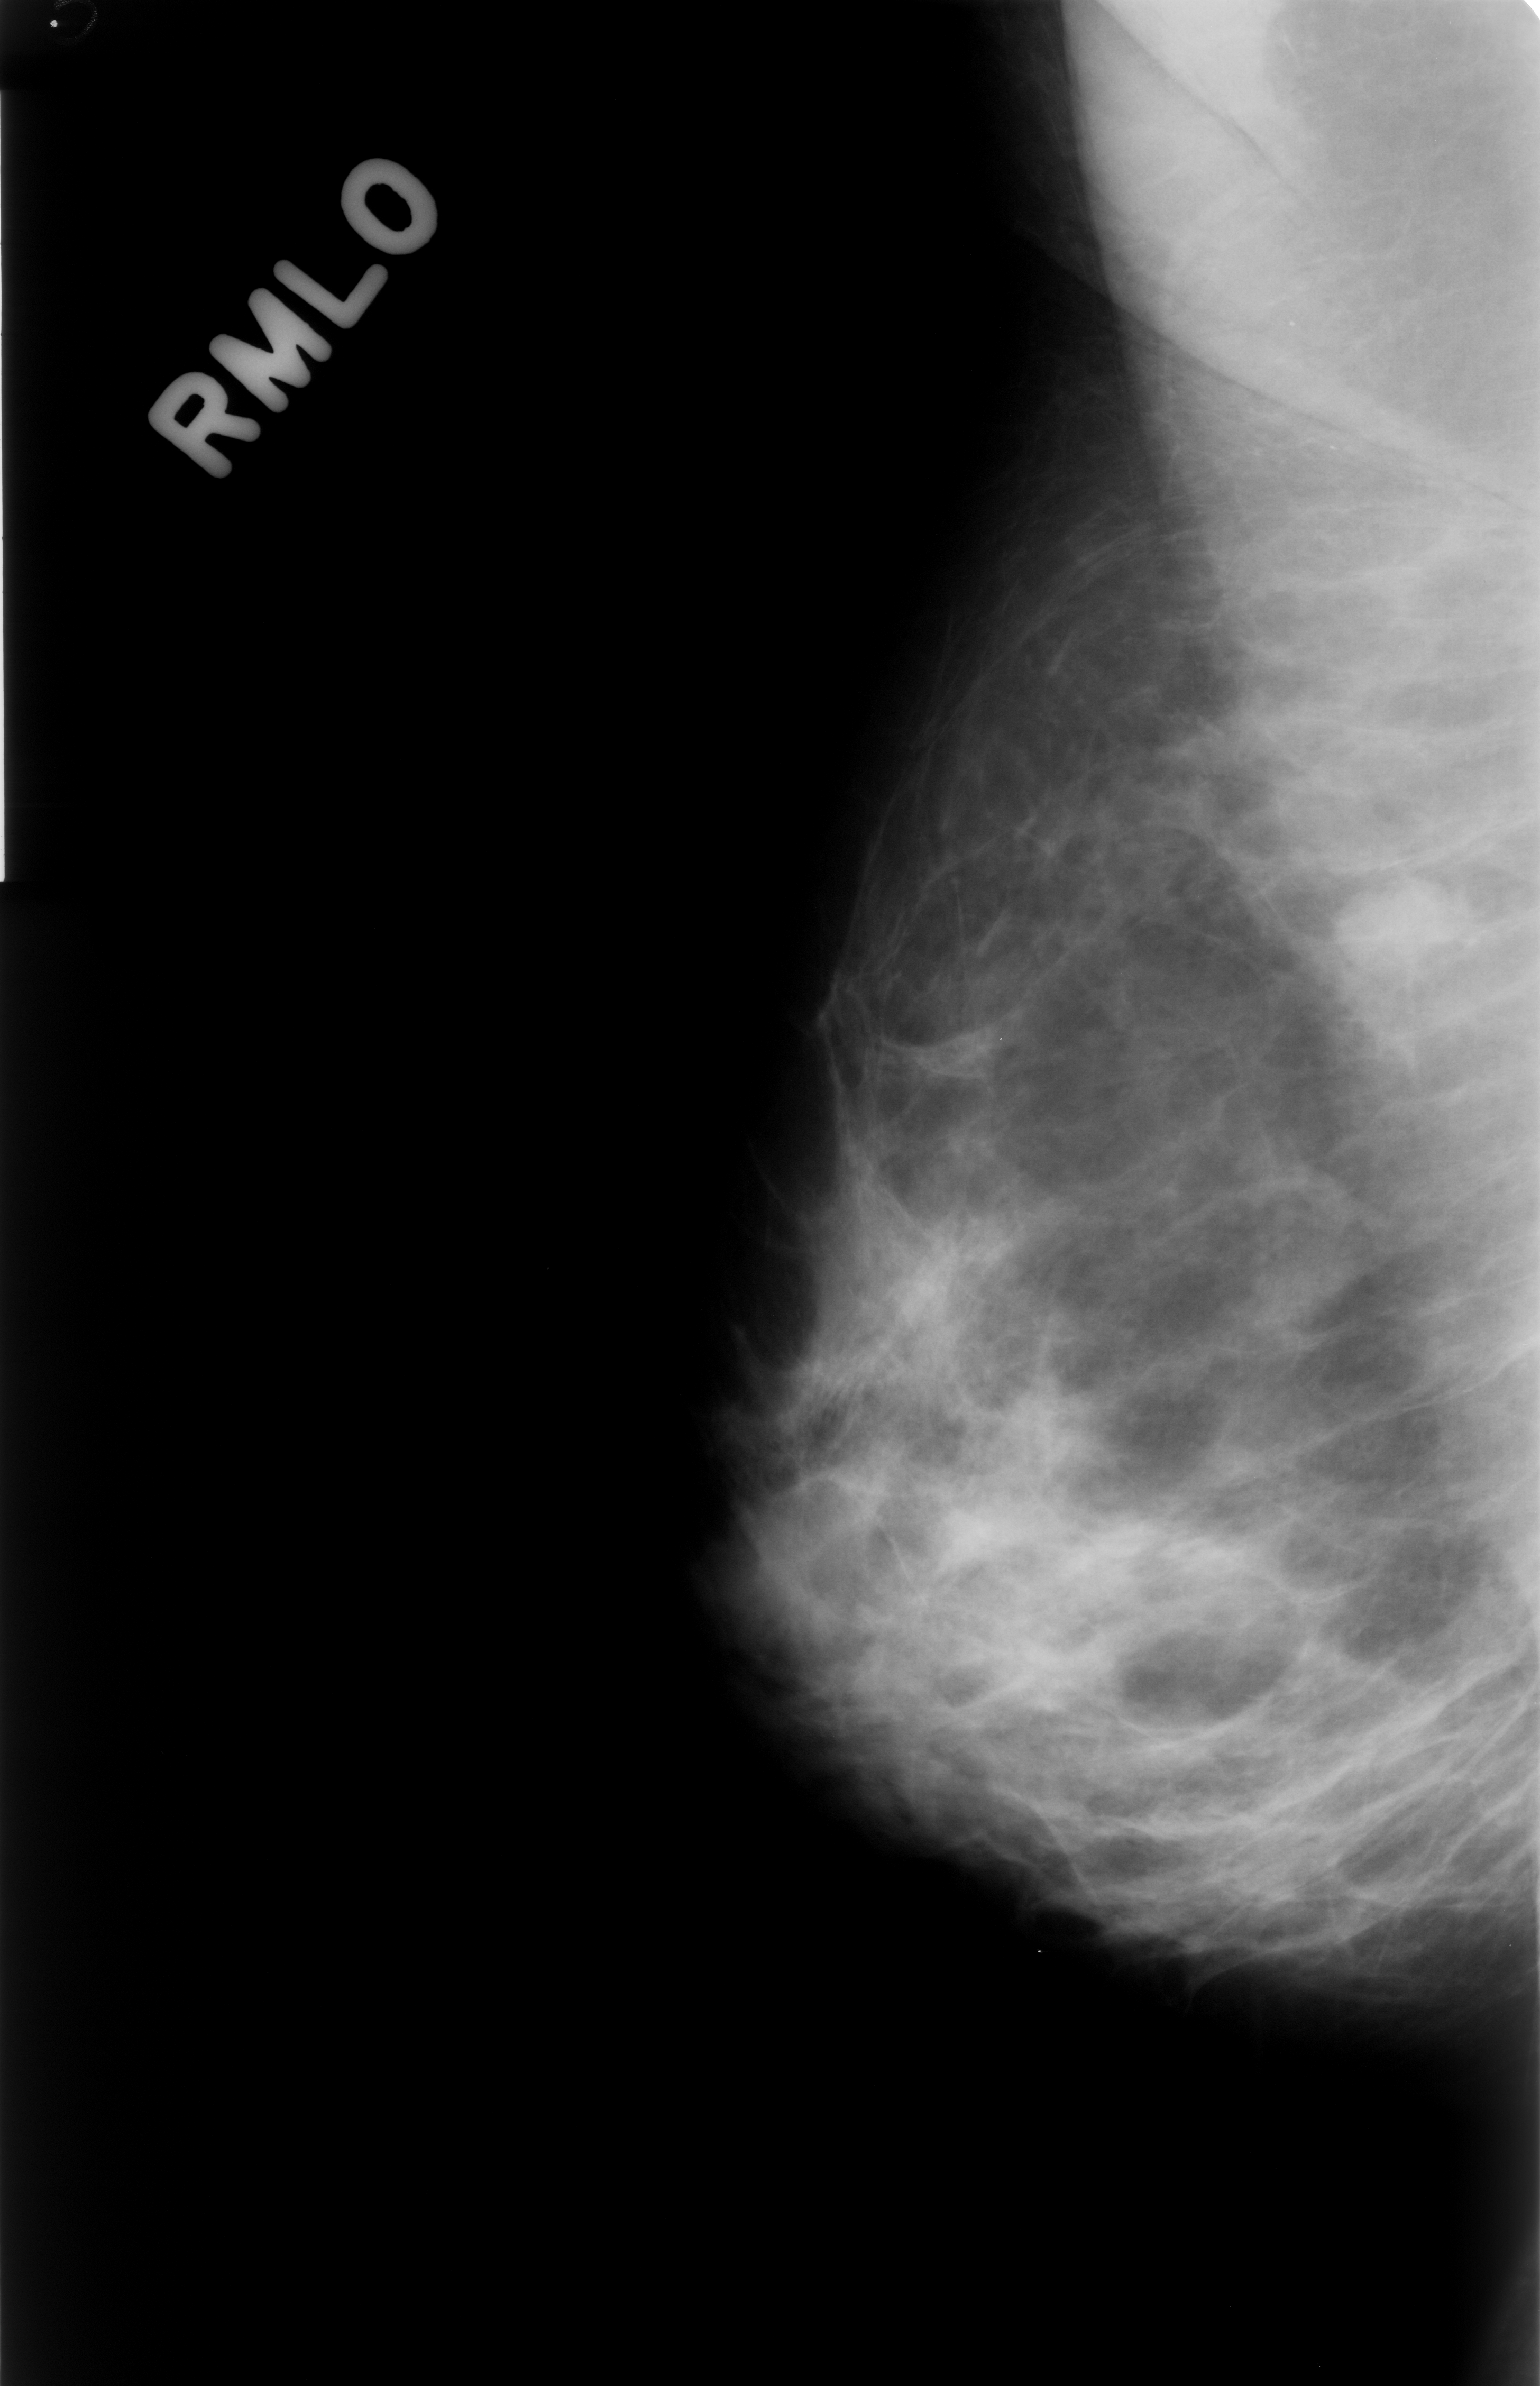
Mammogram (digitized film), right breast, MLO view, BI-RADS breast density category 3 (scale 1–4).
- Marked findings (only marked abnormalities are described; nothing is implied about the rest of the image): mass, shape oval, margins circumscribed; BI-RADS assessment category 4; subtlety rating 4 on a 1 (subtle) to 5 (obvious) scale; pathology result (as recorded, not read from the image): benign.